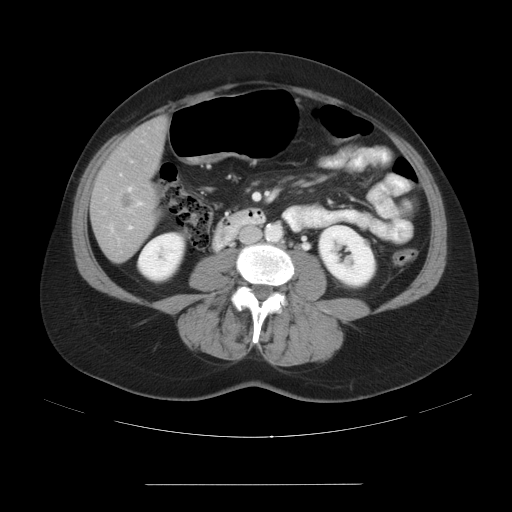
Contrast-enhanced abdominal CT, one axial slice; position 6 of 27 along the scan axis; 120 kVp; intravenous contrast given; soft-tissue window (W 400 / L 40 HU); 7.5 mm slice thickness; 512 × 512 image matrix, field of view 440 × 440 mm. Female patient, age 58 years. From the clinical record (not read from this slice): diagnosis: colorectal cancer liver metastases, imaged before liver resection; multiple liver metastases: yes; largest metastasis: 1.9 cm; disease in both lobes: yes.
Annotated regions visible in this slice (expert manual segmentation):
- hepatic veins: box from (x=128, y=188) to (x=132, y=191) px
- liver: (x=92, y=120)–(x=165, y=262)
- planned liver remnant (the part of the liver to remain after resection): (x=98, y=120)–(x=165, y=188)
- portal vein (with intrahepatic branches): (x=109, y=141)–(x=144, y=233)
- liver metastasis: (x=119, y=192)–(x=136, y=209)